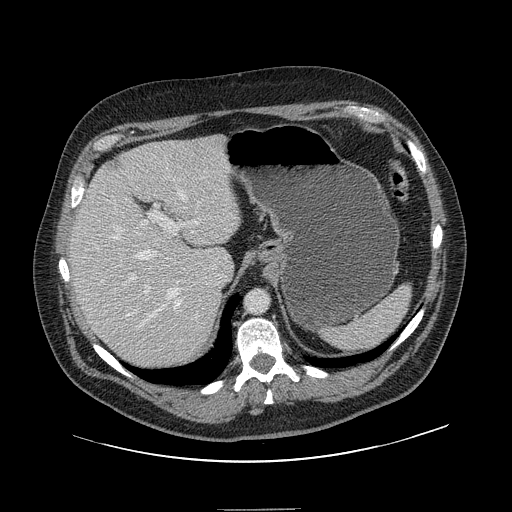
Contrast-enhanced abdominal CT, one axial slice; slice 109 of 154 in the series (ordered by position); intravenous contrast given; soft-tissue window (W 400 / L 40 HU); 2.5 mm slice thickness; 512 × 512 image matrix, field of view 451 × 451 mm. Male patient, age 61 years. From the clinical record (not read from this slice): diagnosis: colorectal cancer liver metastases, imaged before liver resection; multiple liver metastases: yes; largest metastasis: 2.6 cm; disease in both lobes: yes.
Outlined on this slice (outlined manually by an expert reader):
- hepatic veins: bounding box [x1, y1, x2, y2] px = [111, 190, 188, 327]
- liver: [70, 137, 241, 369]
- planned liver remnant (the part of the liver to remain after resection): [70, 144, 242, 359]
- portal vein (with intrahepatic branches): [121, 203, 199, 317]